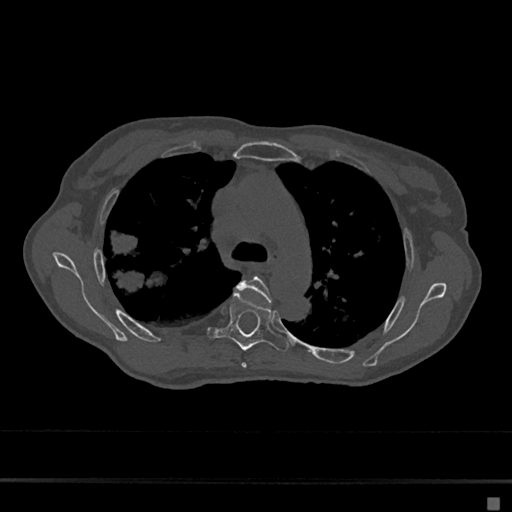
CT including the spine, one axial slice; position 470 of 797 along the scan axis; reconstruction kernel Br40s/3; bone window (W 1800 / L 400 HU); 0.5 mm slice thickness; 512 × 512 image matrix, field of view 360 × 360 mm. Female patient, age 68 years. Case-level facts recorded for this patient, not image findings: primary cancer: renal.
Structures marked on this image (semi-automatic segmentation, software-assisted and operator-edited):
- T4 vertebra: bounding box [x1, y1, x2, y2] px = [236, 276, 272, 368]
- T5 vertebra: [209, 292, 288, 351]